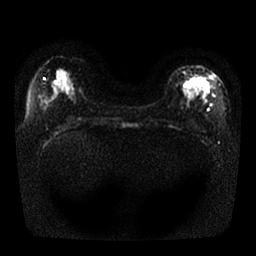
Breast MRI, one axial slice. Slice 13 of 25 in the series (ordered by position). Diffusion-weighted series; image 2 of 4 stored at this slice position (different b-values; order by instance number). 1.5 T. 4 mm slice thickness. 256 × 256 image matrix, field of view 330 × 330 mm. Female patient.
Annotated regions visible in this slice (outlined manually by an expert reader):
- tumour on diffusion-weighted imaging: bounding box [x1, y1, x2, y2] px = [184, 79, 202, 92]